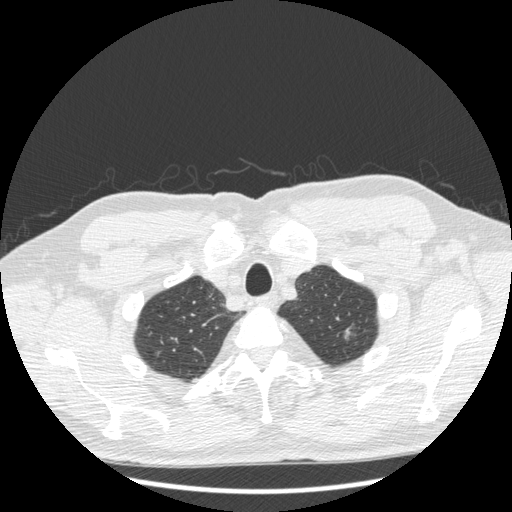
Axial slice from a low-dose chest CT screening exam. Third screening round (two years after baseline). Lung window (W 1500 / L -600 HU). 1.25 mm slice thickness. Standard (soft-tissue) reconstruction kernel (STANDARD). Slice 32 of 223 in the series. Male participant, aged 69 years at enrolment. Former smoker at enrolment.
Expert reader's lesion annotation, bounding box <328,318,364,345> (left, top, right, bottom; pixels). Screening reader's record for this exam (one nodule recorded; not confirmed to be the boxed lesion): non-calcified nodule or mass ≥4 mm, left upper lobe, 7 × 6 mm, smooth margins, soft tissue attenuation, pre-existing on the prior screen: yes; interval growth: yes.